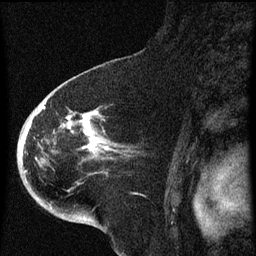
Breast MRI (dynamic contrast-enhanced), one sagittal slice; position 42 of 60 along the scan axis; dynamic contrast-enhanced series, image 2 of 4 at this slice position (ordered by acquisition); 1.5 T; TE 4.2 ms, TR 8 ms; 2 mm slice thickness; 256 × 256 image matrix. Female patient, age 71 years.
Outlined on this slice (semi-automatic segmentation, software-assisted and operator-edited):
- analysis volume of interest (the breast-tissue region the enhancement analysis was run in; not a lesion): bounding box (x1, y1, x2, y2) in pixels: (32, 86, 133, 205)
- tumour enhancement mask (voxels above the 70 % enhancement threshold inside the analysis volume of interest): (39, 106, 117, 157)